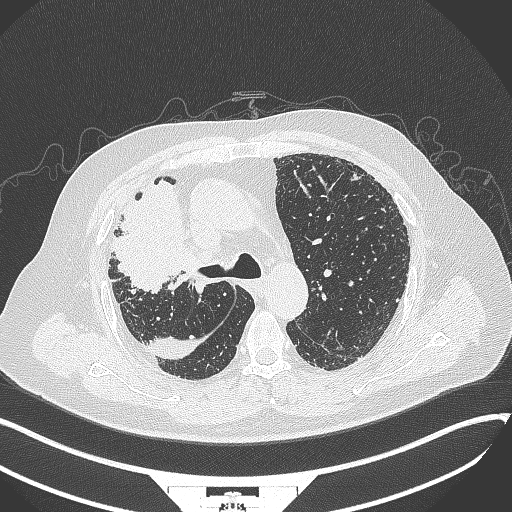
Chest CT, one axial slice; slice 242 of 384 in the series (ordered by position); reconstruction kernel B70f; 120 kVp; lung window (W 1500 / L -600 HU); 512 × 512 image matrix, field of view 400 × 400 mm. Patient: male, 69 years. Case-level facts recorded for this patient, not image findings: clinical TNM (as recorded): T4 N3 M1.
Structures marked on this image (bounding box drawn by a radiologist):
- lung tumour (recorded histology: adenocarcinoma): box from (x=102, y=174) to (x=200, y=293) px